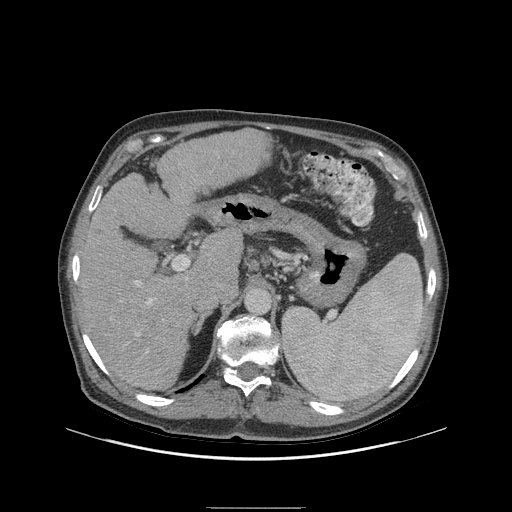
Contrast-enhanced abdominal CT (liver protocol), one axial slice; 140 kVp; soft-tissue window (W 400 / L 40 HU); 2.5 mm slice thickness; 512 × 512 image matrix, field of view 440 × 440 mm. Case-level facts recorded for this patient, not image findings: diagnosis: hepatocellular carcinoma (patient treated with transarterial chemoembolisation; whether this scan precedes or follows treatment is not stated here); TNM stage (as recorded): Stage-I; Child-Pugh class: A; tumour nodularity: uninodular; tumour size: 5.1 cm.
Annotated regions visible in this slice (semi-automatically segmented with operator editing):
- liver parenchyma outside the tumour (the mass and vessels are separate outlines, so this box may not span the whole liver): bounding box <78,136,247,388> (left, top, right, bottom; pixels)
- liver vessels: <104,278,188,371>